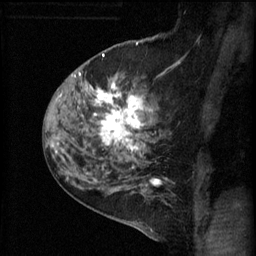
Breast MRI (dynamic contrast-enhanced), one sagittal slice; slice 40 of 60 in the series (ordered by position); 3 images stored at this slice position (order not interpretable as contrast timing); 1.5 T; TE 4.2 ms, TR 11 ms; 256 × 256 image matrix. Female patient, age 52 years.
Annotated regions visible in this slice (semi-automatic segmentation, software-assisted and operator-edited):
- analysis volume of interest (the breast-tissue region the enhancement analysis was run in; not a lesion): bounding box (x1, y1, x2, y2) in pixels: (86, 76, 165, 157)
- tumour enhancement mask (voxels above the 70 % enhancement threshold inside the analysis volume of interest): (93, 82, 145, 153)